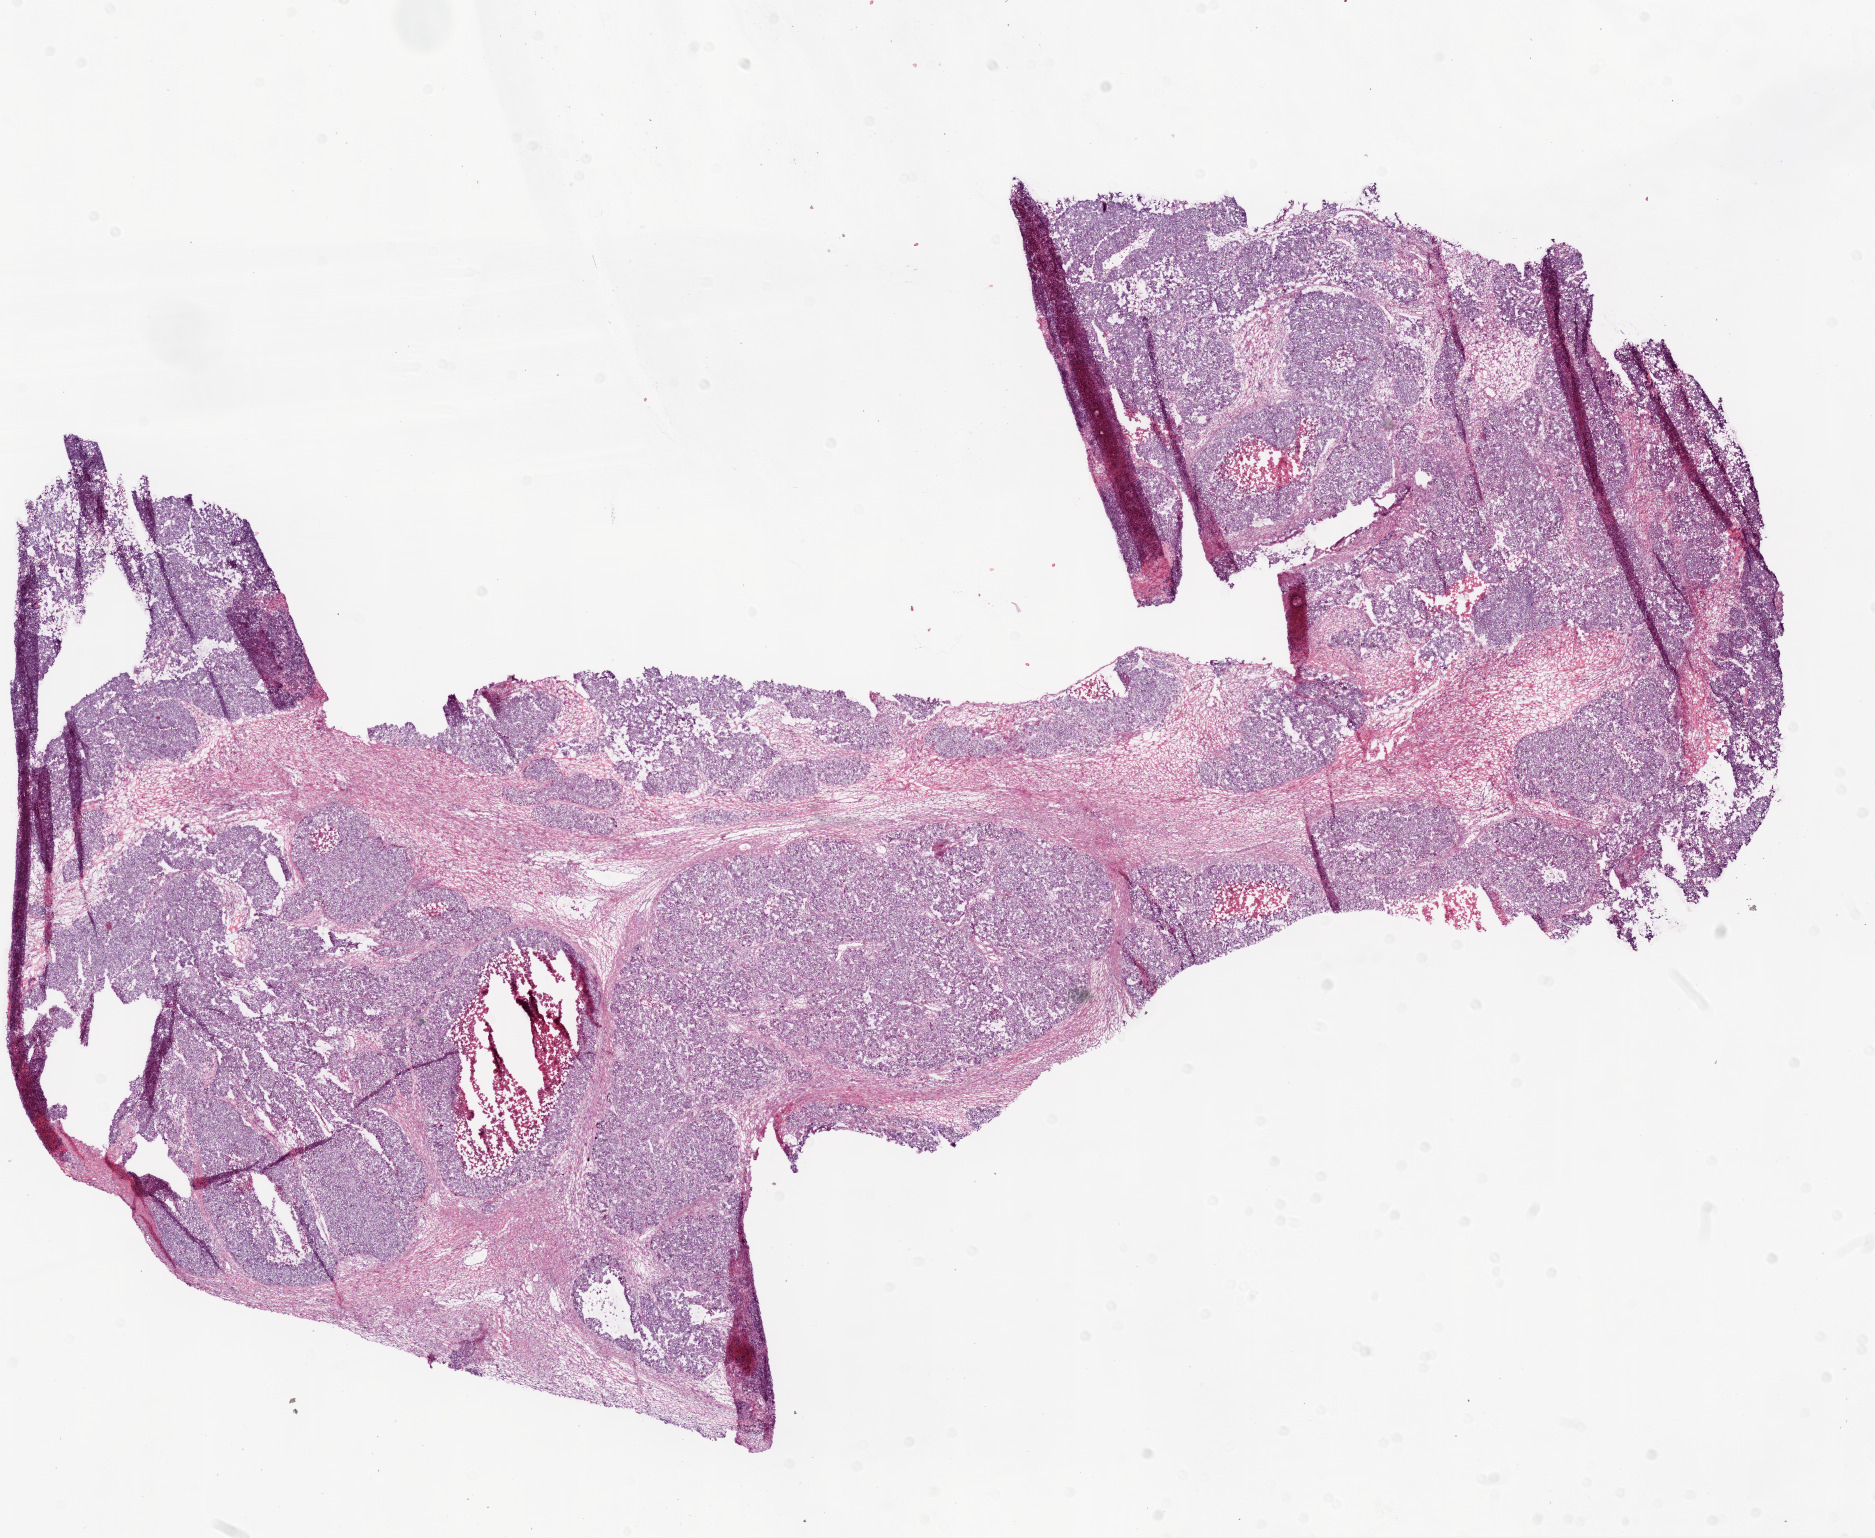
H&E whole-slide image — a low-resolution overview of the entire scanned area, about 15.0 x 12.3 mm; frozen section; sample: primary tumour, ovary. Patient: female, age at initial diagnosis 46 years. Histologic grade: G3 (poorly differentiated). Slide review estimates, as recorded: tumour cells 65%, tumour nuclei 80%, normal cells 0%, stromal cells 33%, necrosis 2%. Inflammatory infiltration, as recorded: lymphocyte infiltration 0%, monocyte infiltration 0%, neutrophil infiltration 0%.
Diagnosis: Serous cystadenocarcinoma, NOS. Laterality: bilateral. FIGO stage: IIIC.